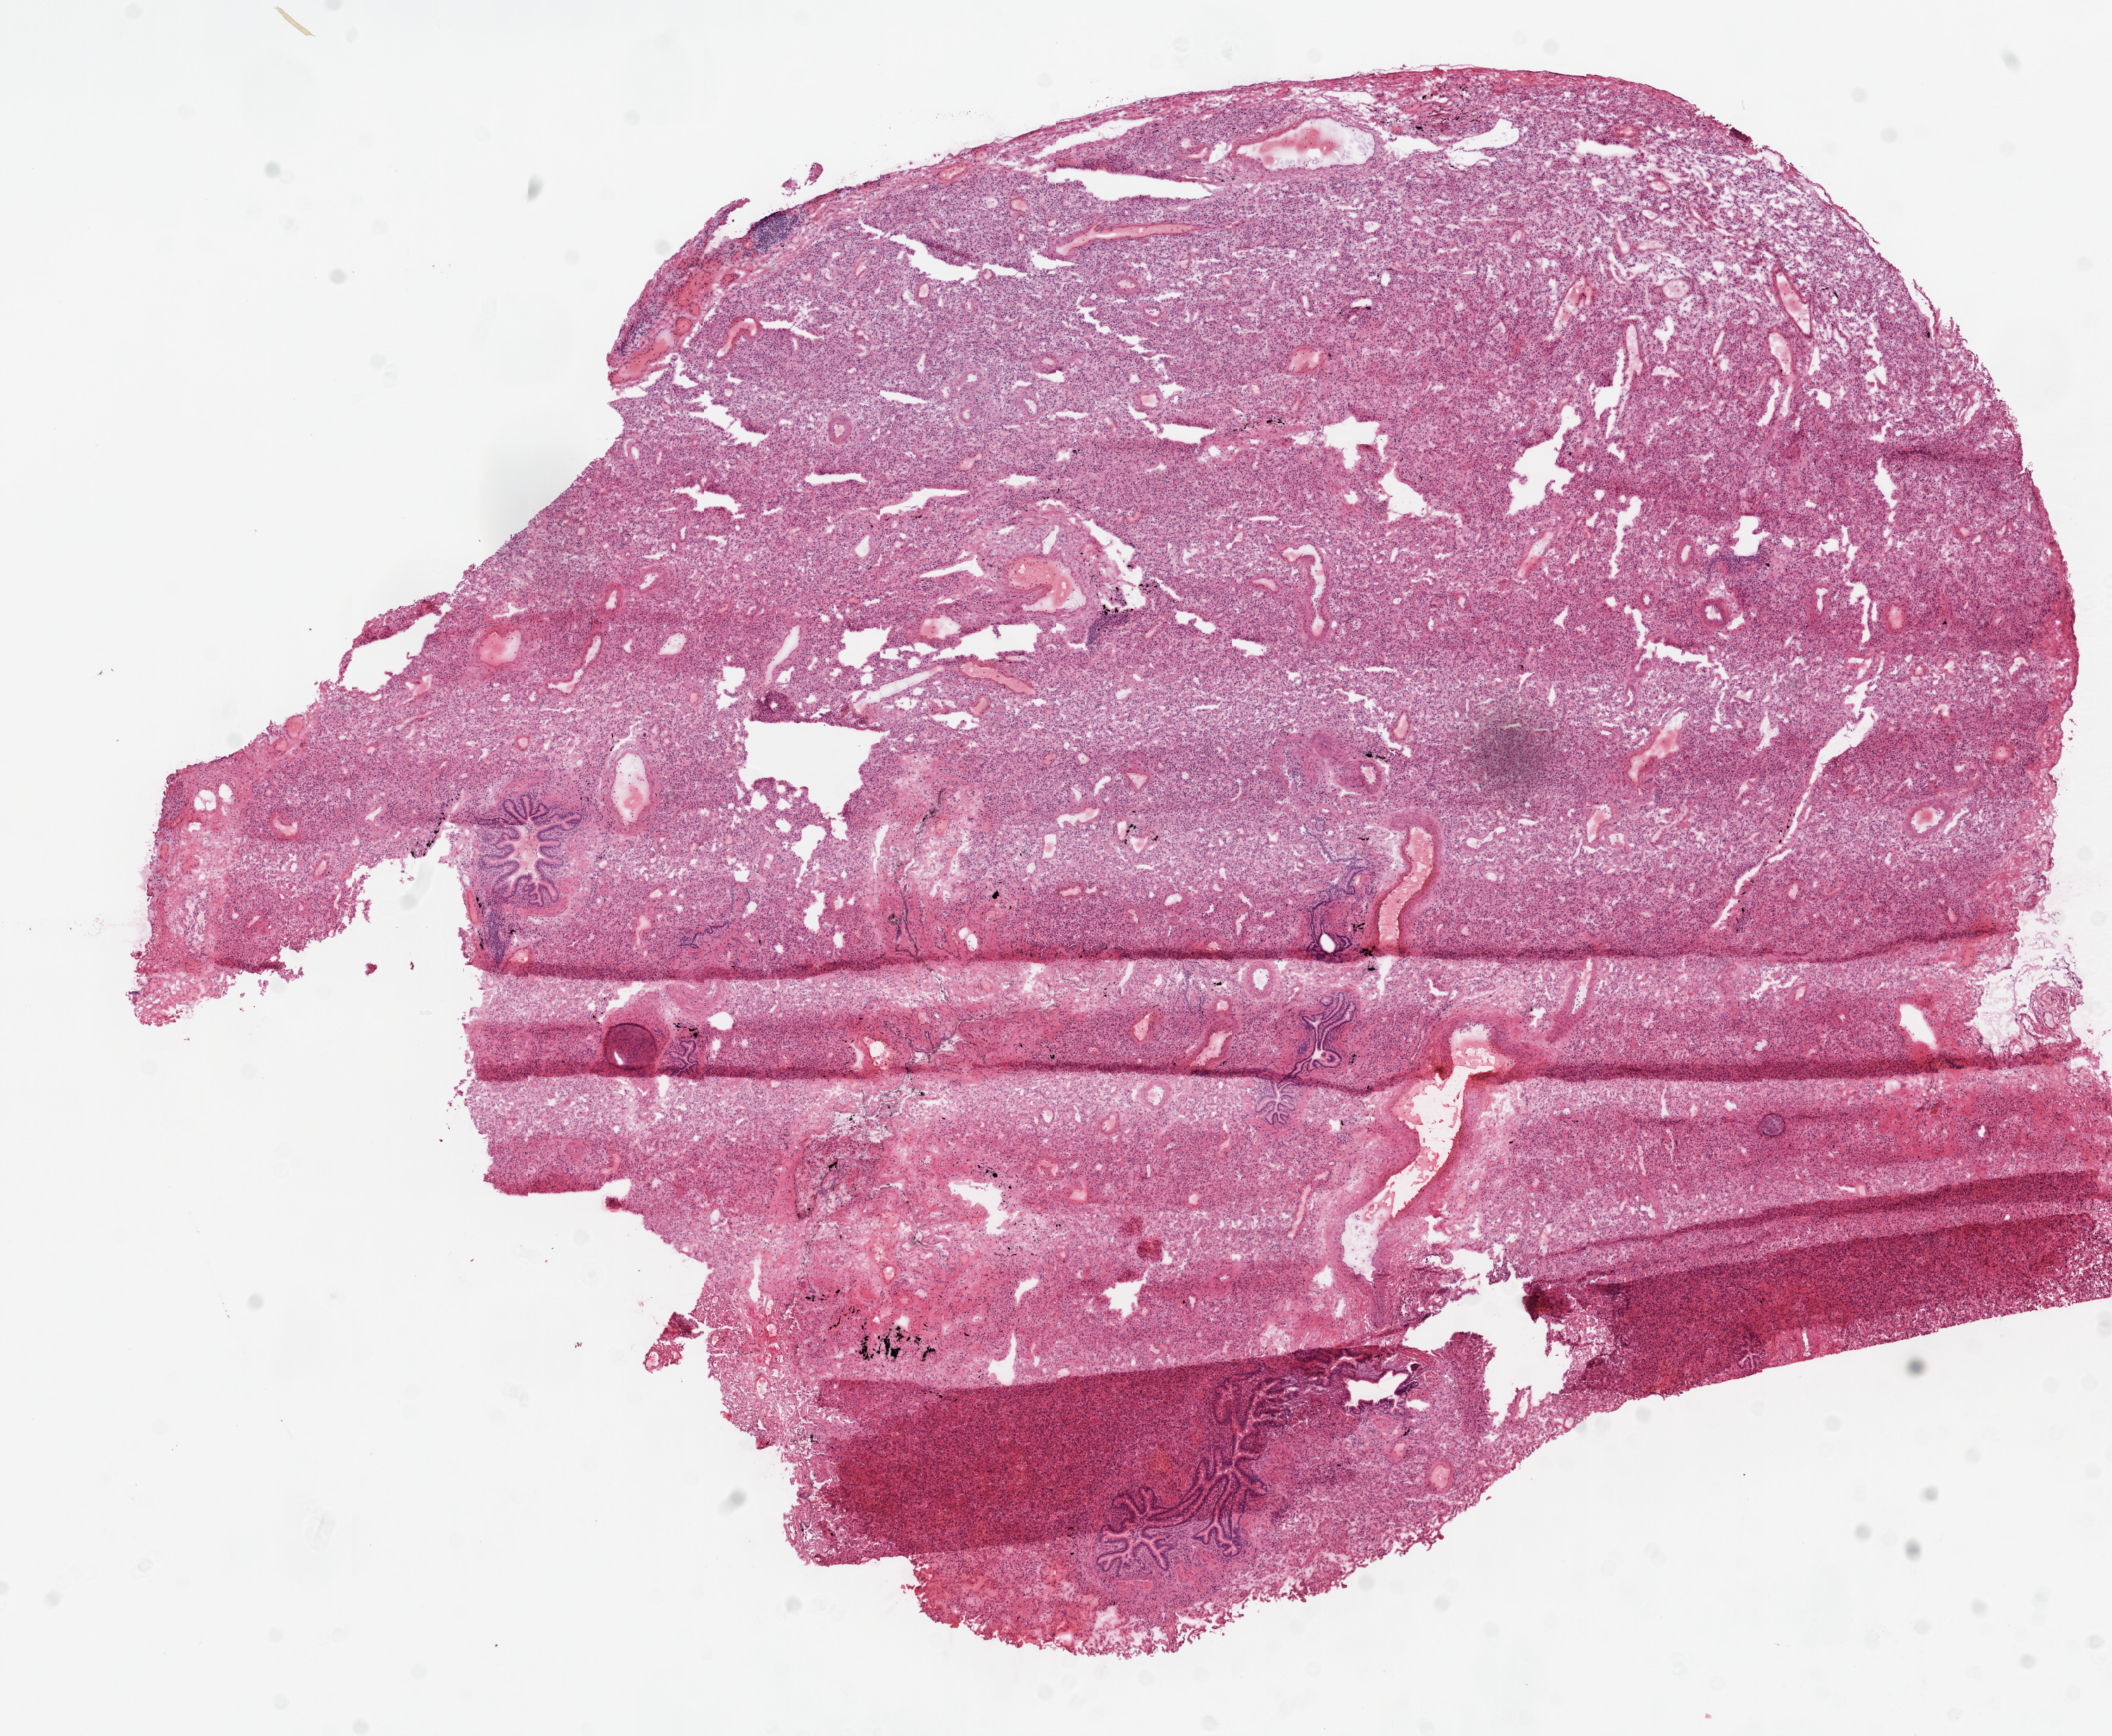
H&E whole-slide image — whole scanned area (about 12.0 x 9.9 mm, slide scanned at 20x) shown as a low-resolution overview. Frozen section. Solid tissue normal (non-tumour tissue) sample from the lung. Male patient; age at initial diagnosis 73 years.
• this section: solid tissue normal (non-tumour) sample from the same patient
• patient diagnosis: Squamous cell carcinoma, NOS (lower lobe, lung)